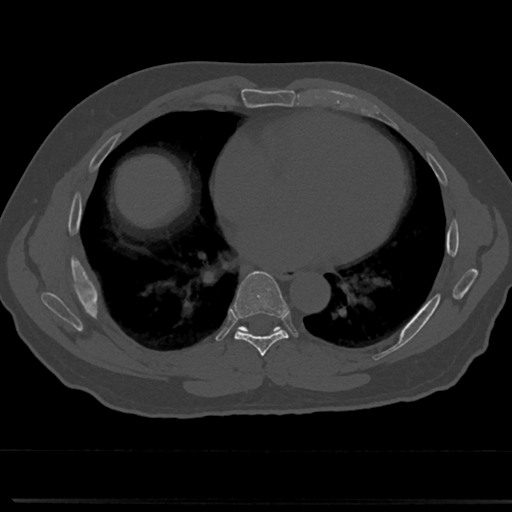
CT including the spine, one axial slice. Slice 395 of 817 in the series (ordered by position). Reconstruction kernel Br40s/3. 120 kVp. Bone window (W 1800 / L 400 HU). 0.5 mm slice thickness. 512 × 512 image matrix, field of view 355 × 355 mm. Male patient, age 61 years. From the clinical record (not read from this slice): primary cancer: prostate.
Annotated regions visible in this slice (semi-automatic segmentation, software-assisted and operator-edited):
- T6 vertebra: bounding box [x1, y1, x2, y2] px = [261, 353, 269, 377]
- T7 vertebra: [214, 275, 310, 357]